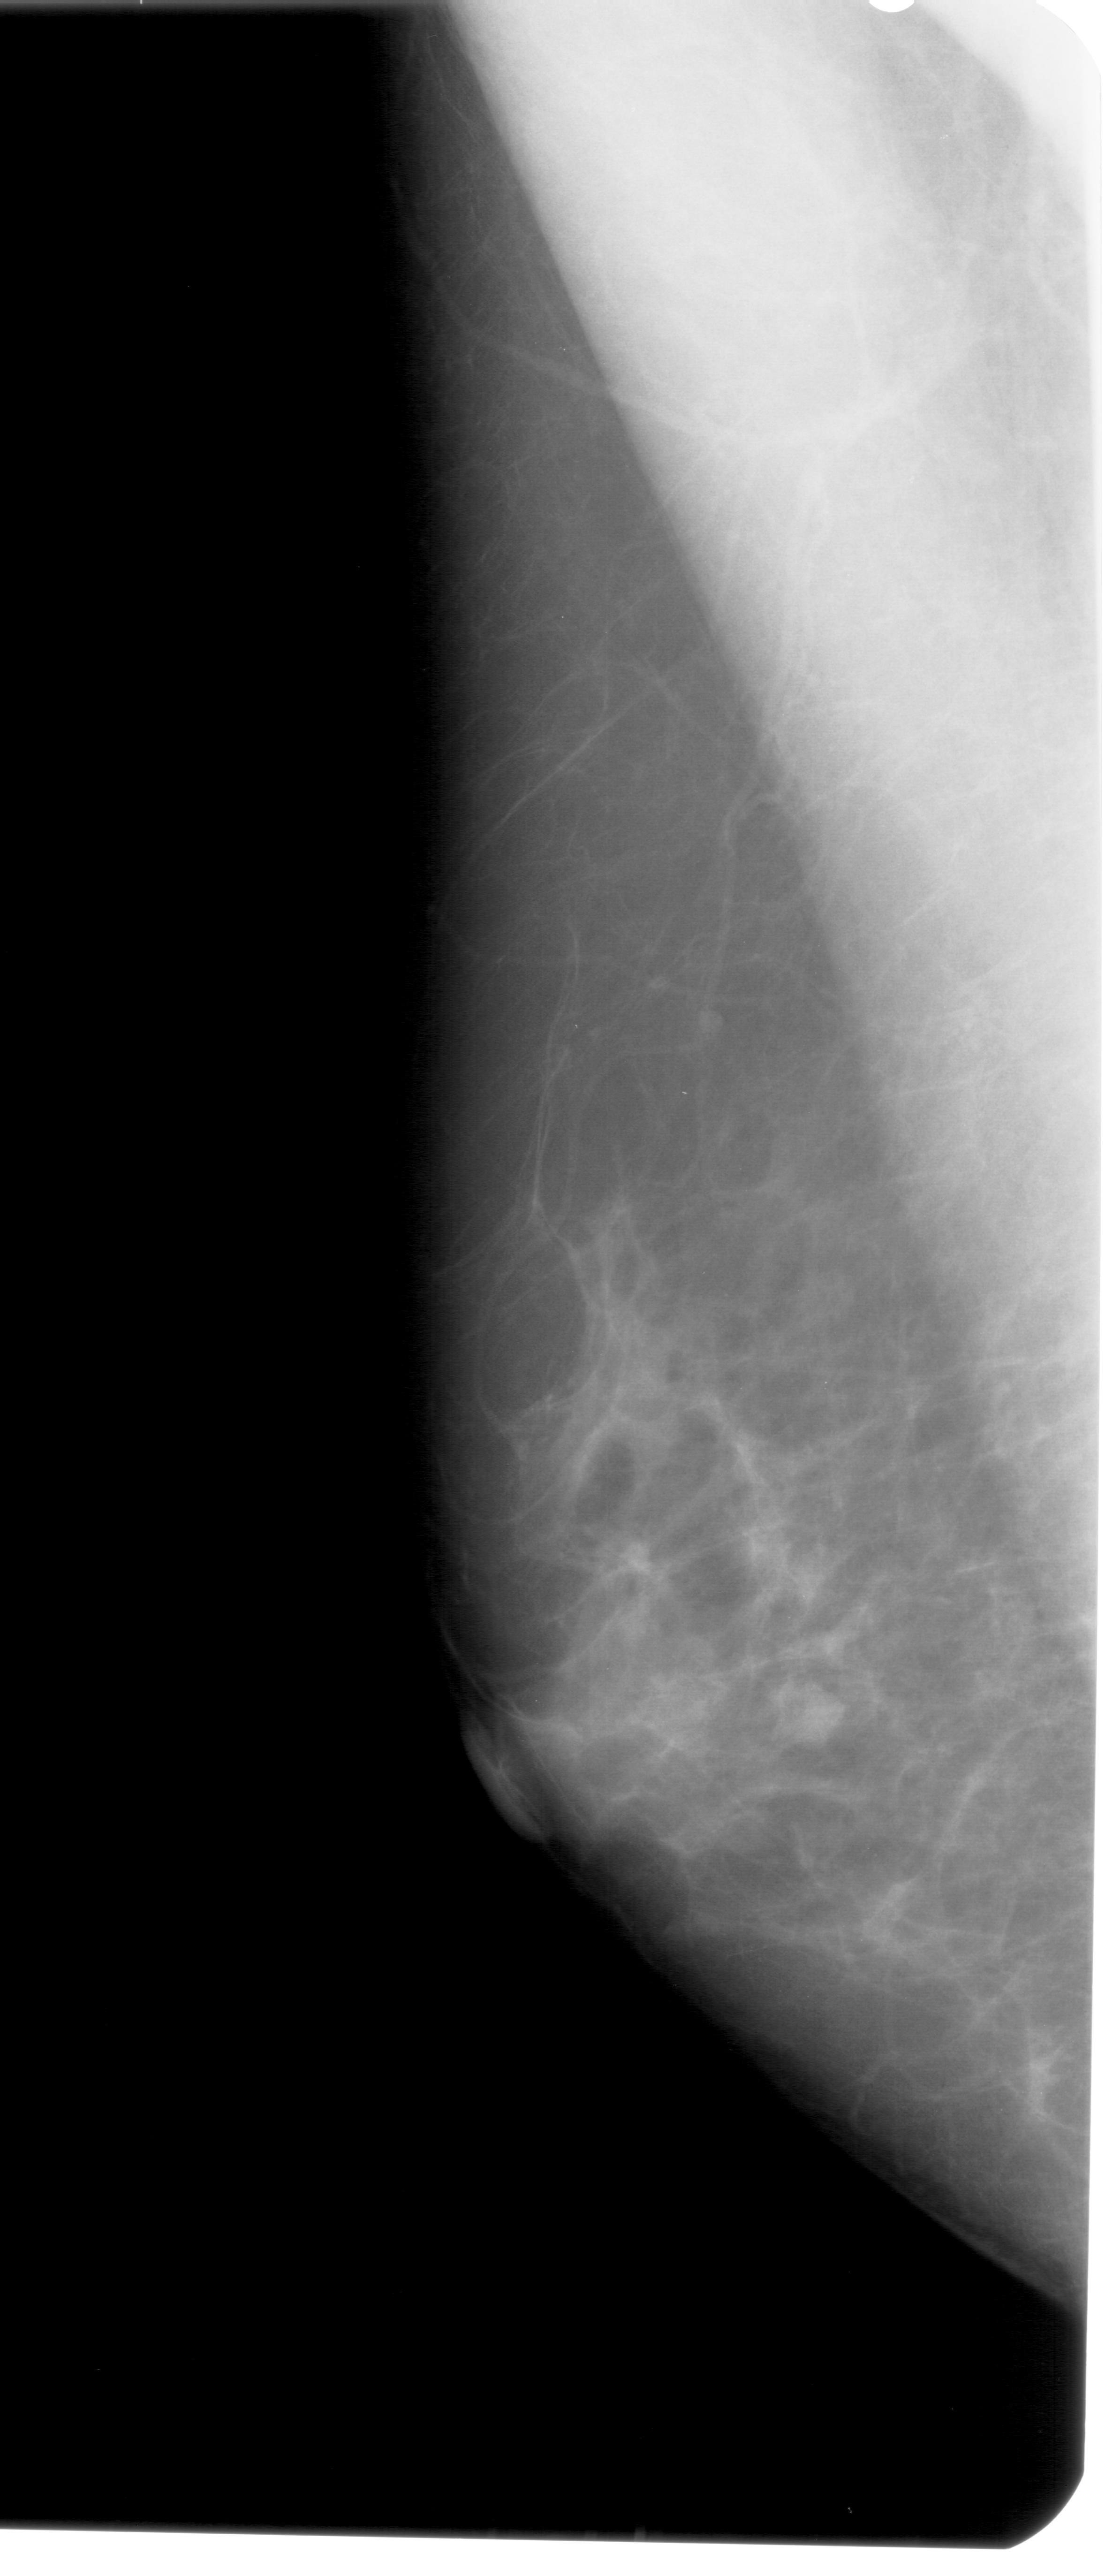
Digitized screen-film mammogram; left breast; mediolateral oblique (MLO) view.
Abnormality record for this image: mass, shape lobulated, margins obscured; BI-RADS assessment category 4; subtlety rating 2 on a 1 (subtle) to 5 (obvious) scale; pathology result (as recorded, not read from the image): benign.